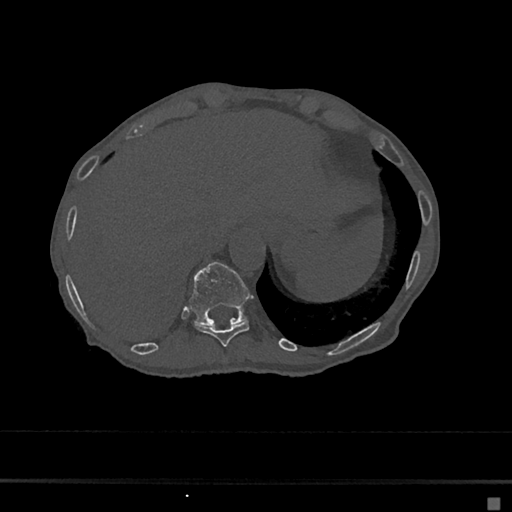
CT including the spine, one axial slice. Position 204 of 797 along the scan axis. 120 kVp. Bone window (W 1800 / L 400 HU). 0.5 mm slice thickness. 512 × 512 image matrix. Female patient, age 68 years. Case-level facts recorded for this patient, not image findings: primary cancer: renal.
Annotated regions visible in this slice (semi-automatic segmentation, software-assisted and operator-edited):
- T10 vertebra: box from (x=195, y=320) to (x=249, y=347) px
- T11 vertebra: (x=190, y=262)–(x=252, y=325)
- T9 vertebra: (x=223, y=359)–(x=226, y=363)